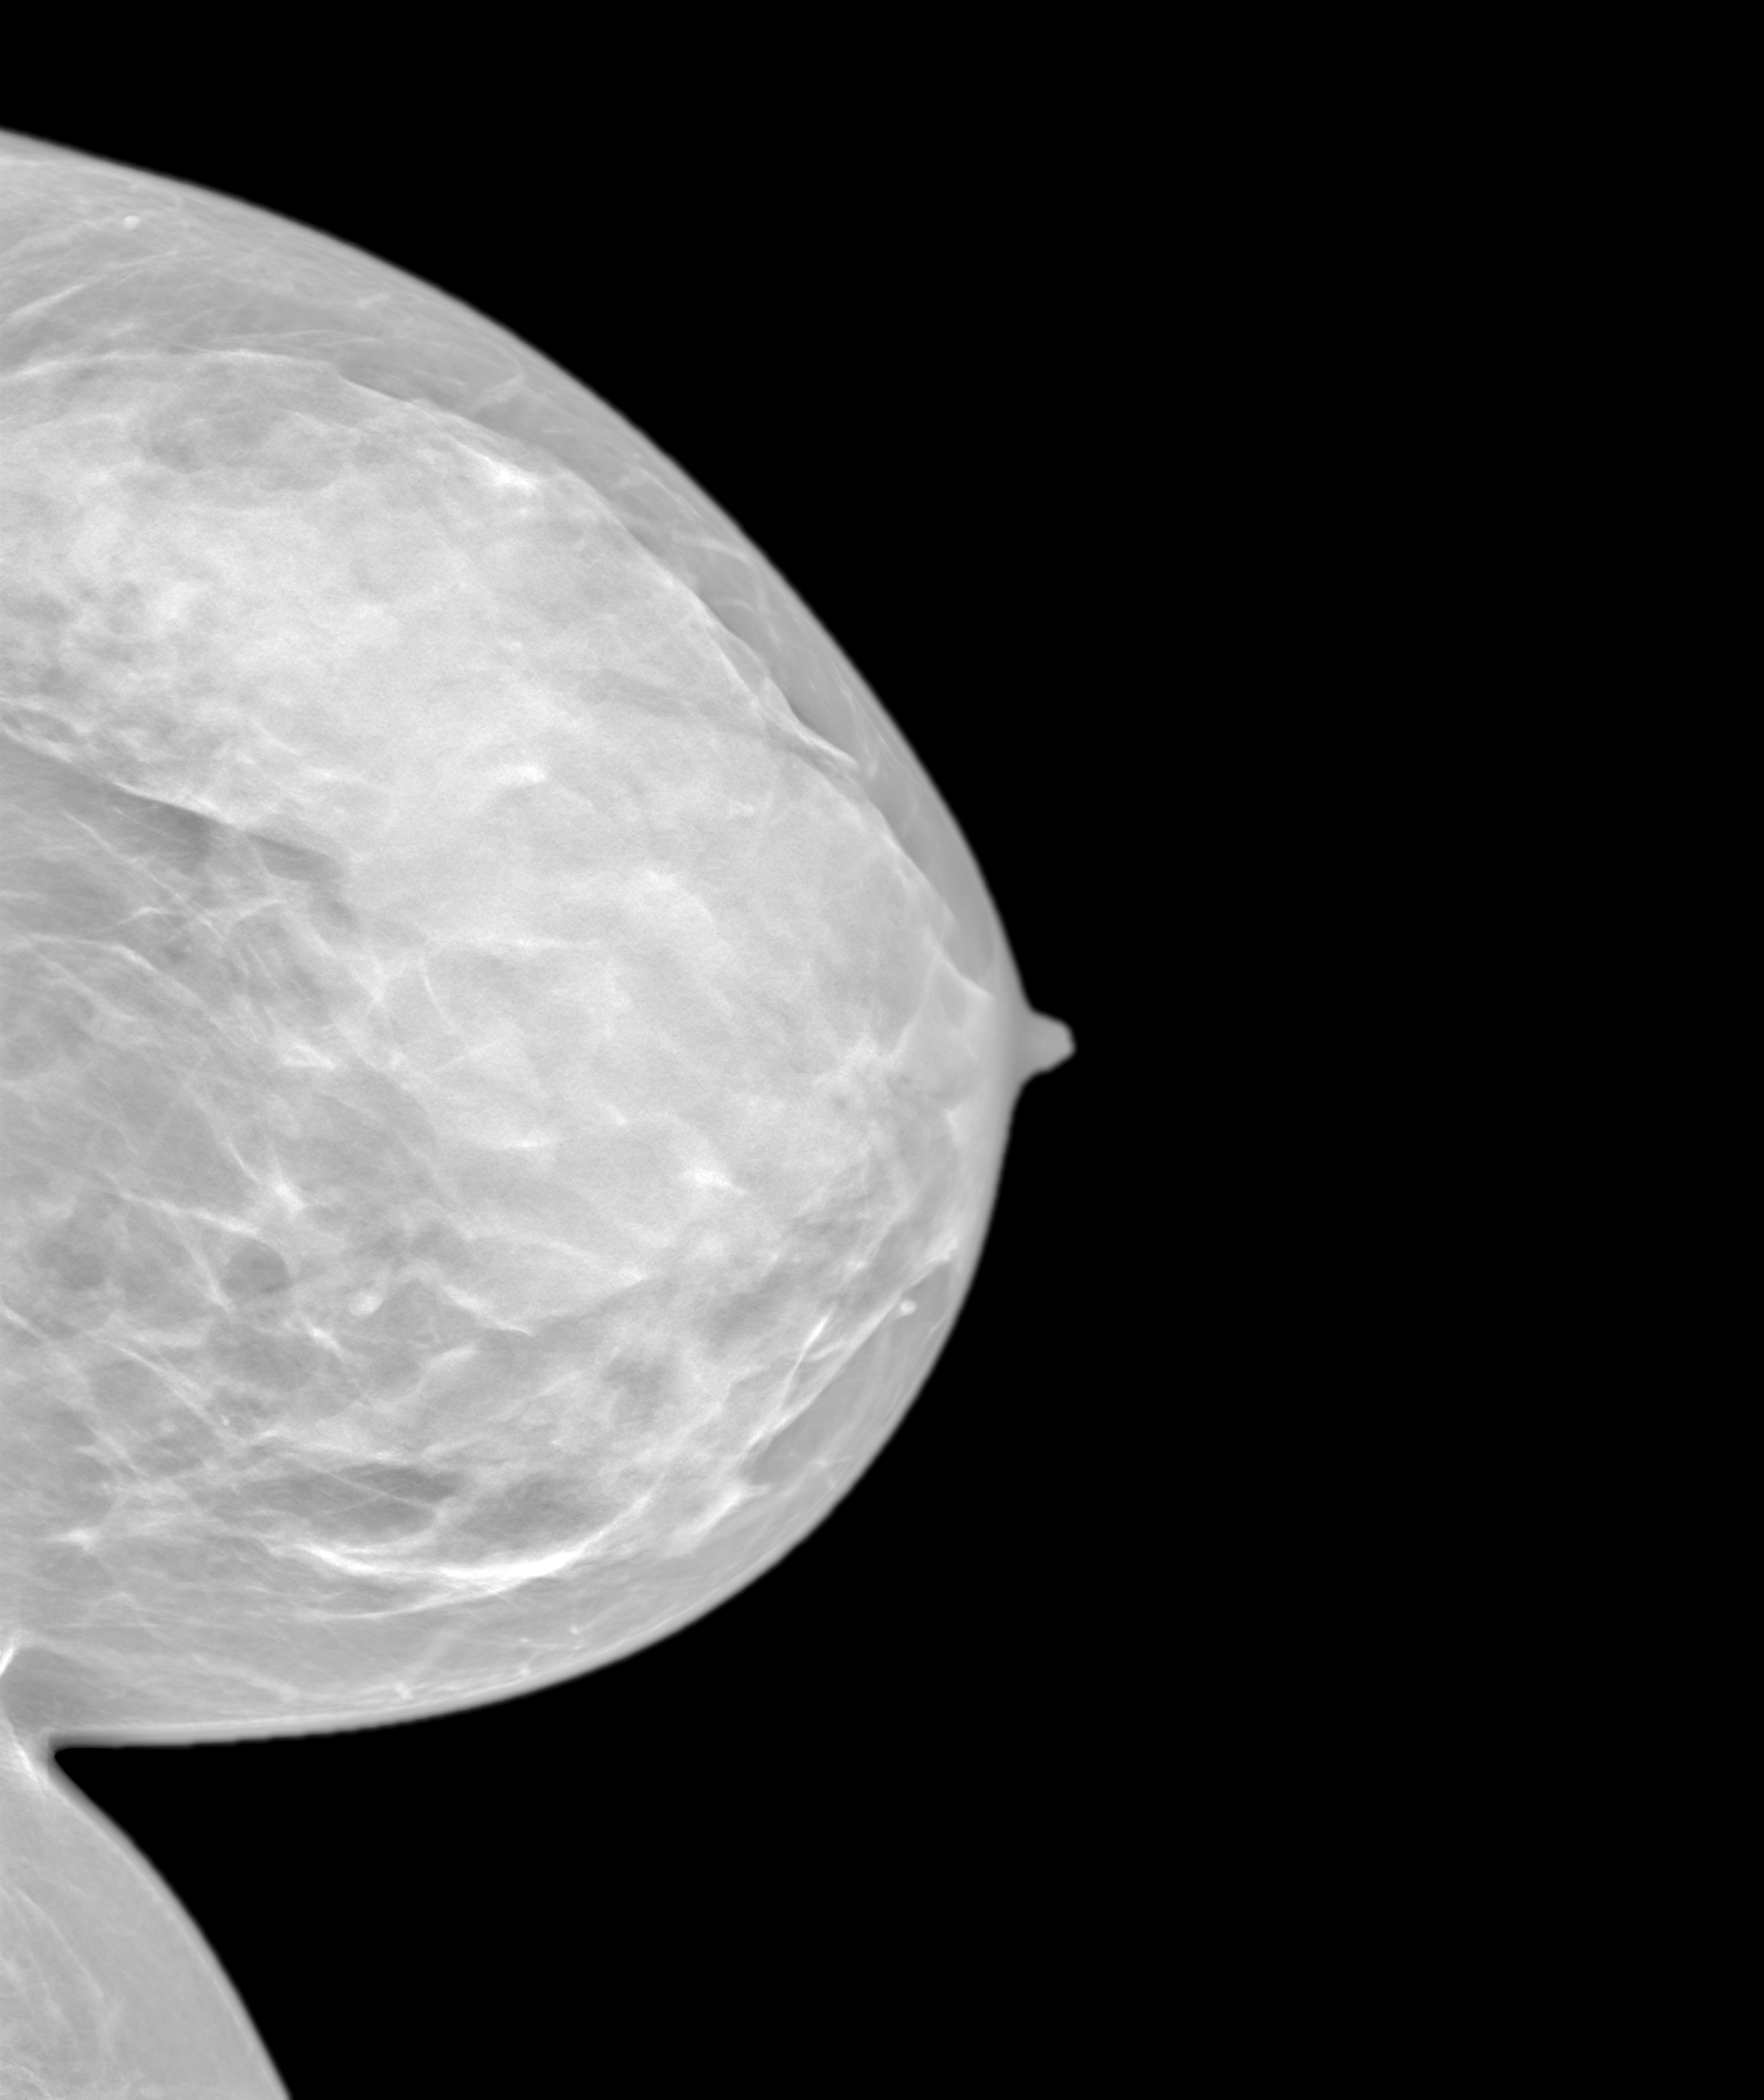
Screening examination. Patient: female, 44 years.
Image type: synthesized 2-D view from tomosynthesis. Breast: left. Projection: cranio-caudal projection.